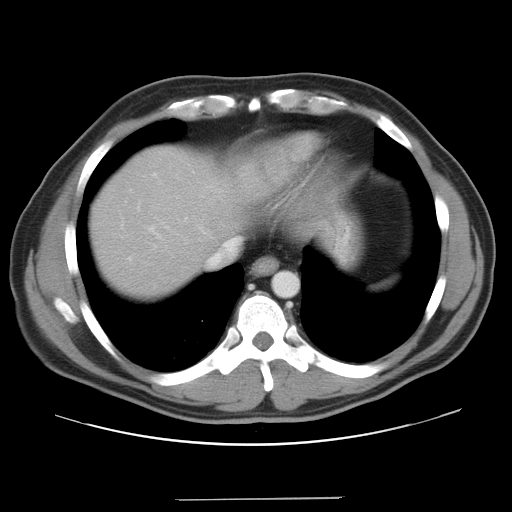
Contrast-enhanced abdominal CT, one axial slice; reconstruction kernel STANDARD; 120 kVp; intravenous contrast given; soft-tissue window (W 400 / L 40 HU); 7.5 mm slice thickness; 512 × 512 image matrix, field of view 400 × 400 mm. Male patient, age 46 years. From the clinical record (not read from this slice): diagnosis: colorectal cancer liver metastases, imaged before liver resection.
Annotated regions visible in this slice (expert manual segmentation):
- hepatic veins: bounding box (x1, y1, x2, y2) in pixels: (207, 237, 241, 267)
- liver: (92, 148, 234, 296)
- planned liver remnant (the part of the liver to remain after resection): (92, 148, 232, 297)
- portal vein (with intrahepatic branches): (153, 173, 157, 177)